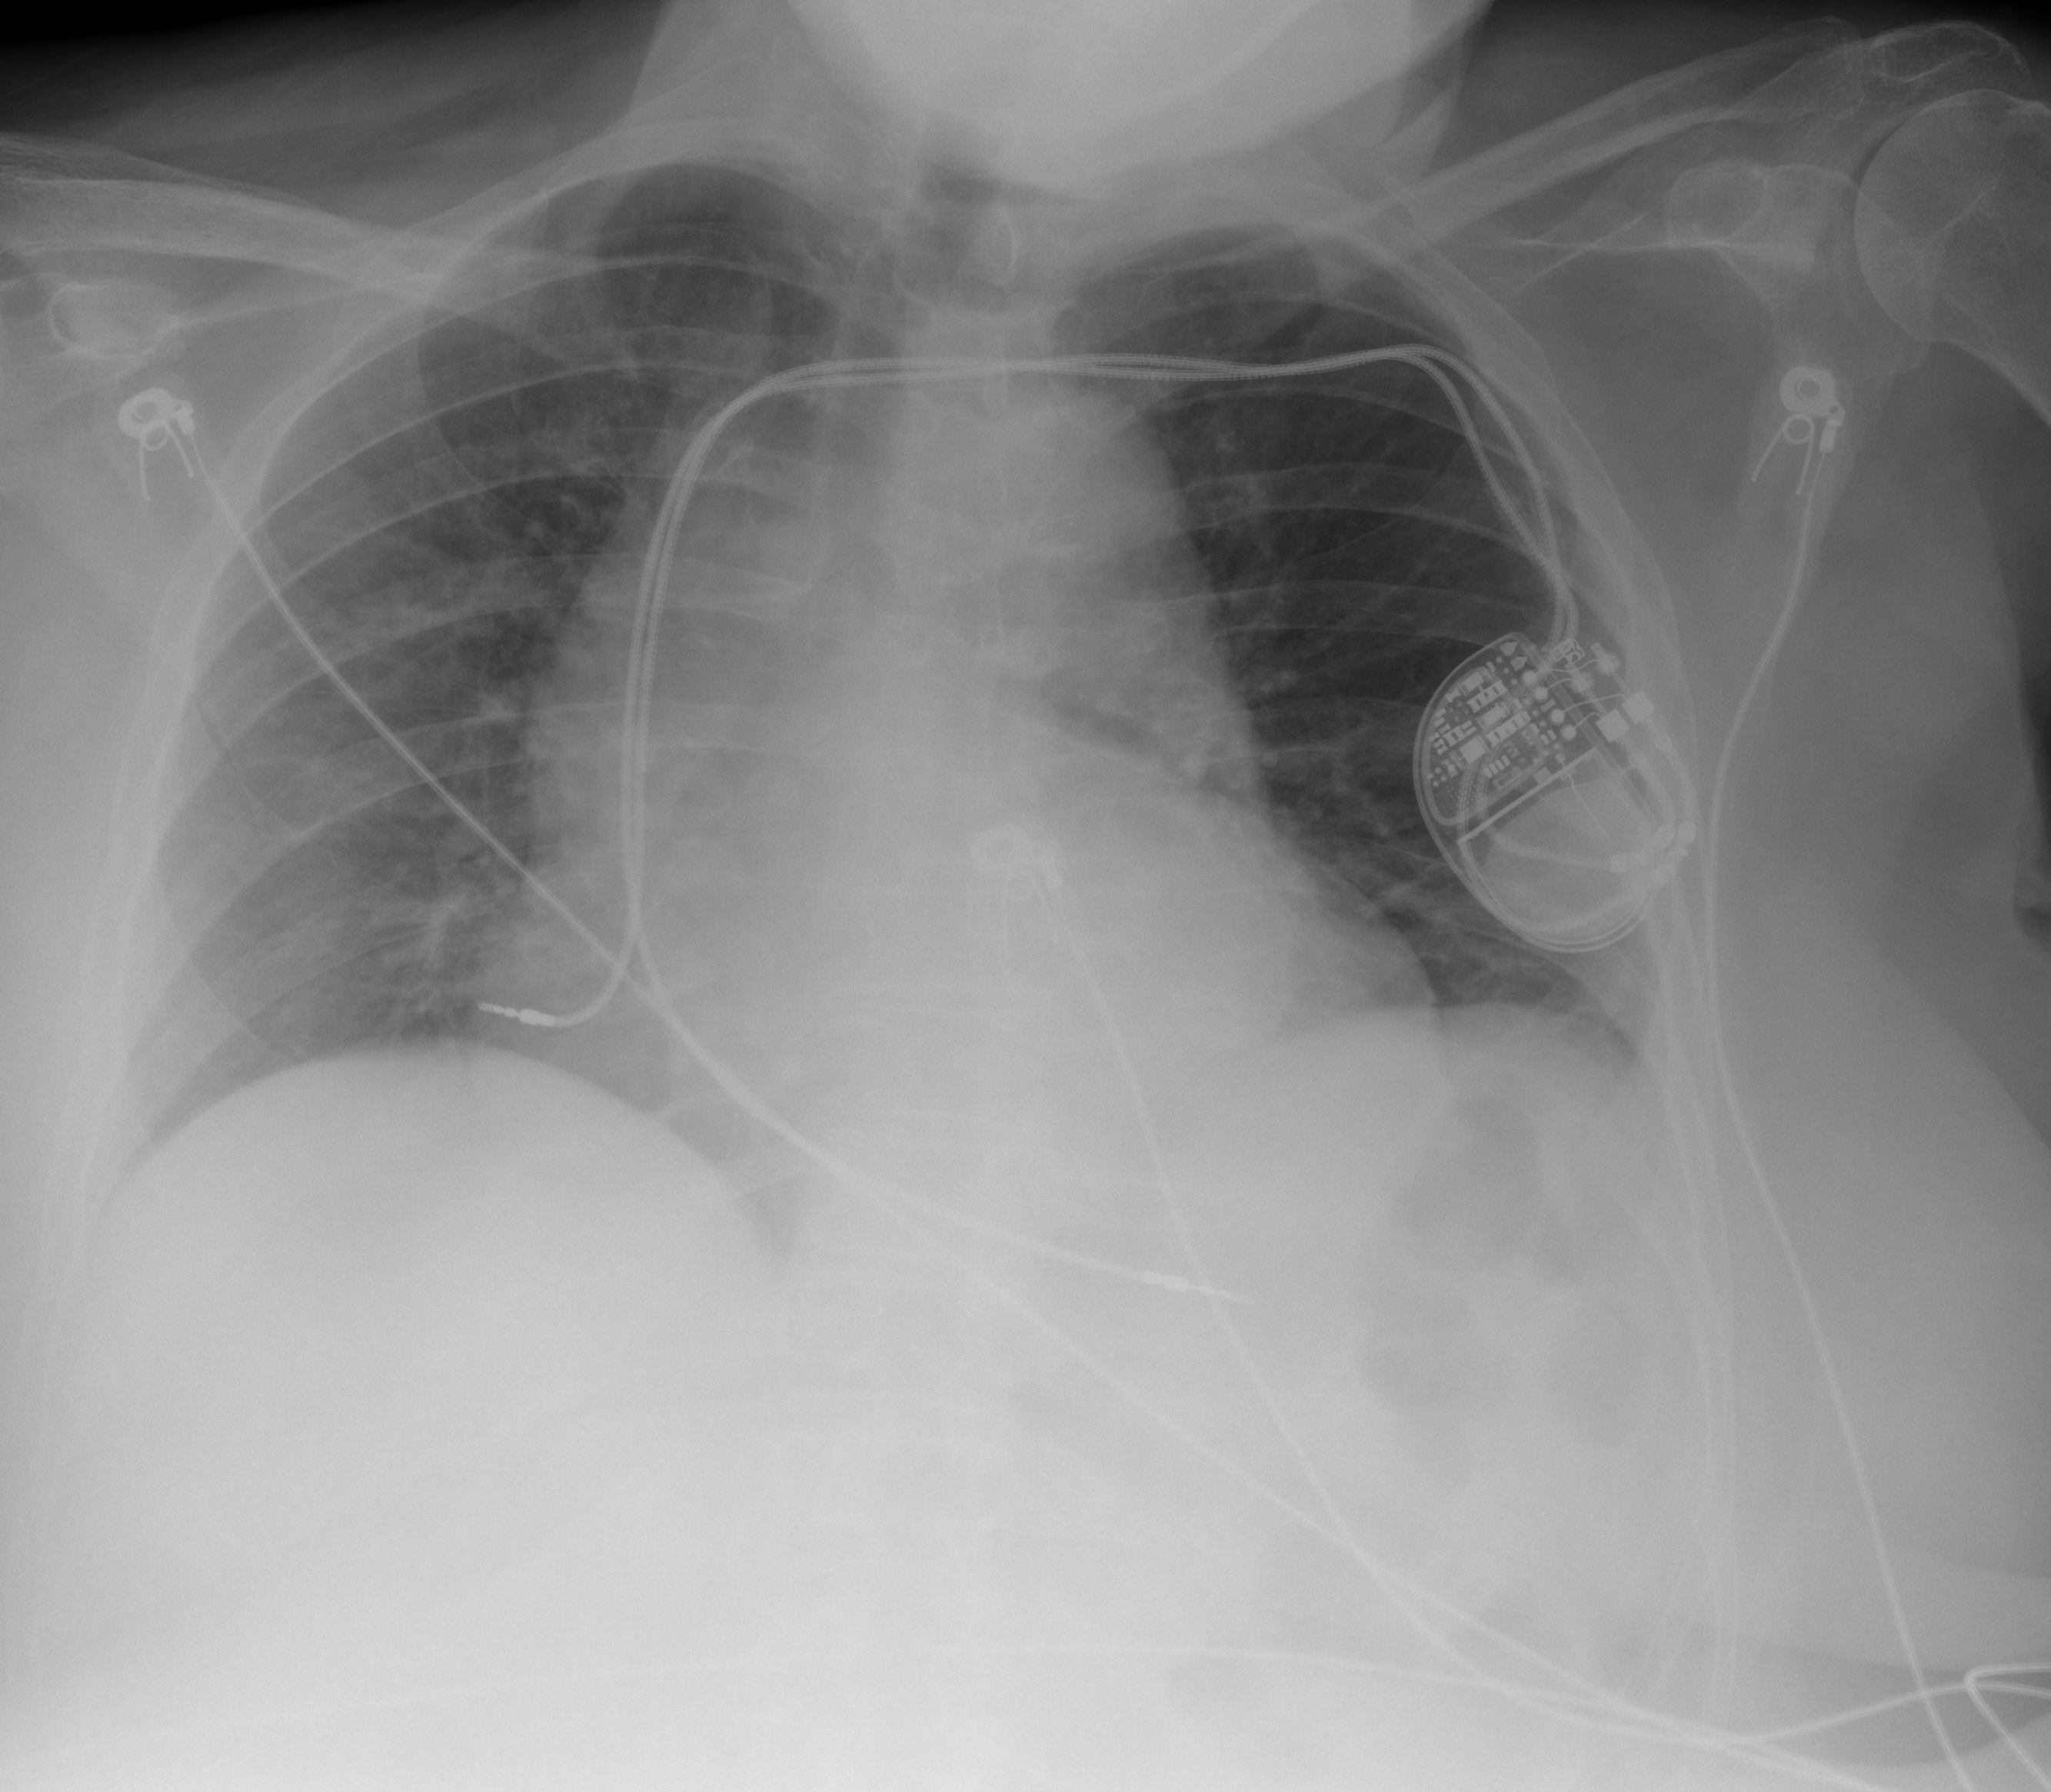
Portable chest radiograph, AP projection. Female patient, age 81 years; imaged 0 days after the COVID-19 diagnosis.
Radiologist key findings (as recorded): Stable appearance of chest, no acute disease.